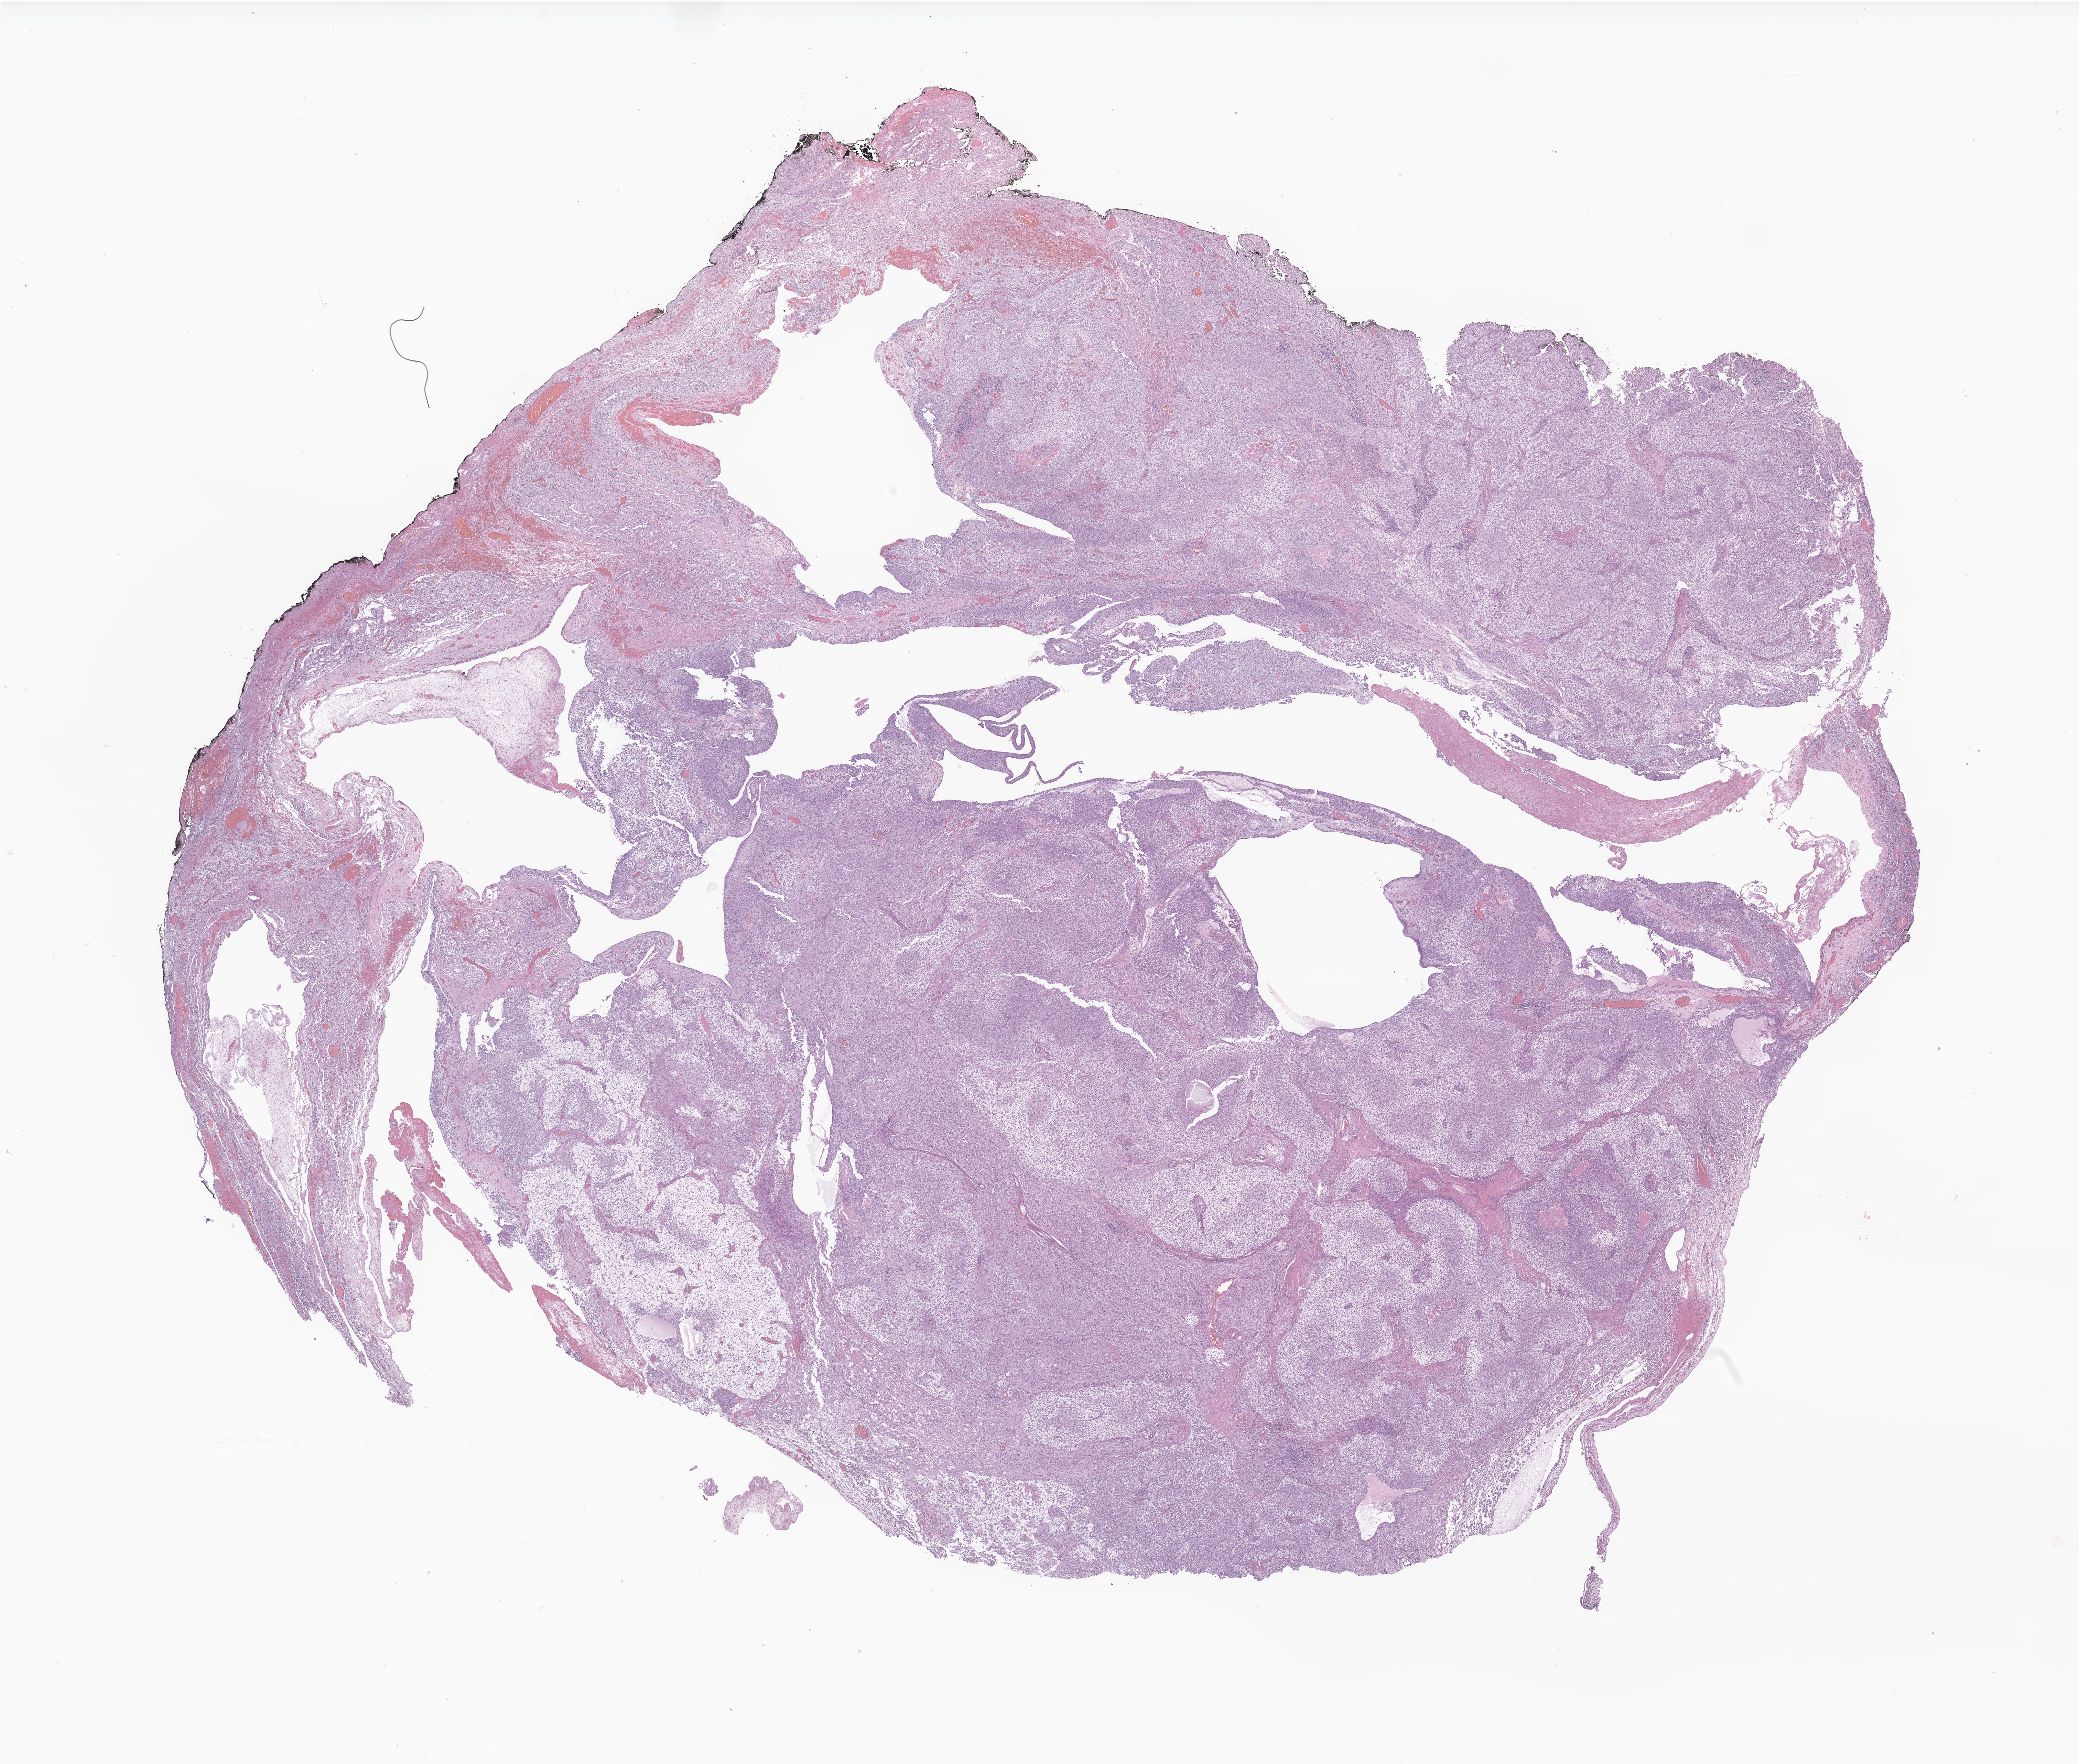
Digitized hematoxylin and eosin (H&E)-stained section of tumor tissue from the brain — whole scanned area (about 25.5 x 21.6 mm) shown as a low-resolution overview, formalin-fixed paraffin-embedded section. Patient: female, age 202 months (16 years 10 months).
* diagnosis (ICD-O-3 morphology term): Neoplasm, malignant